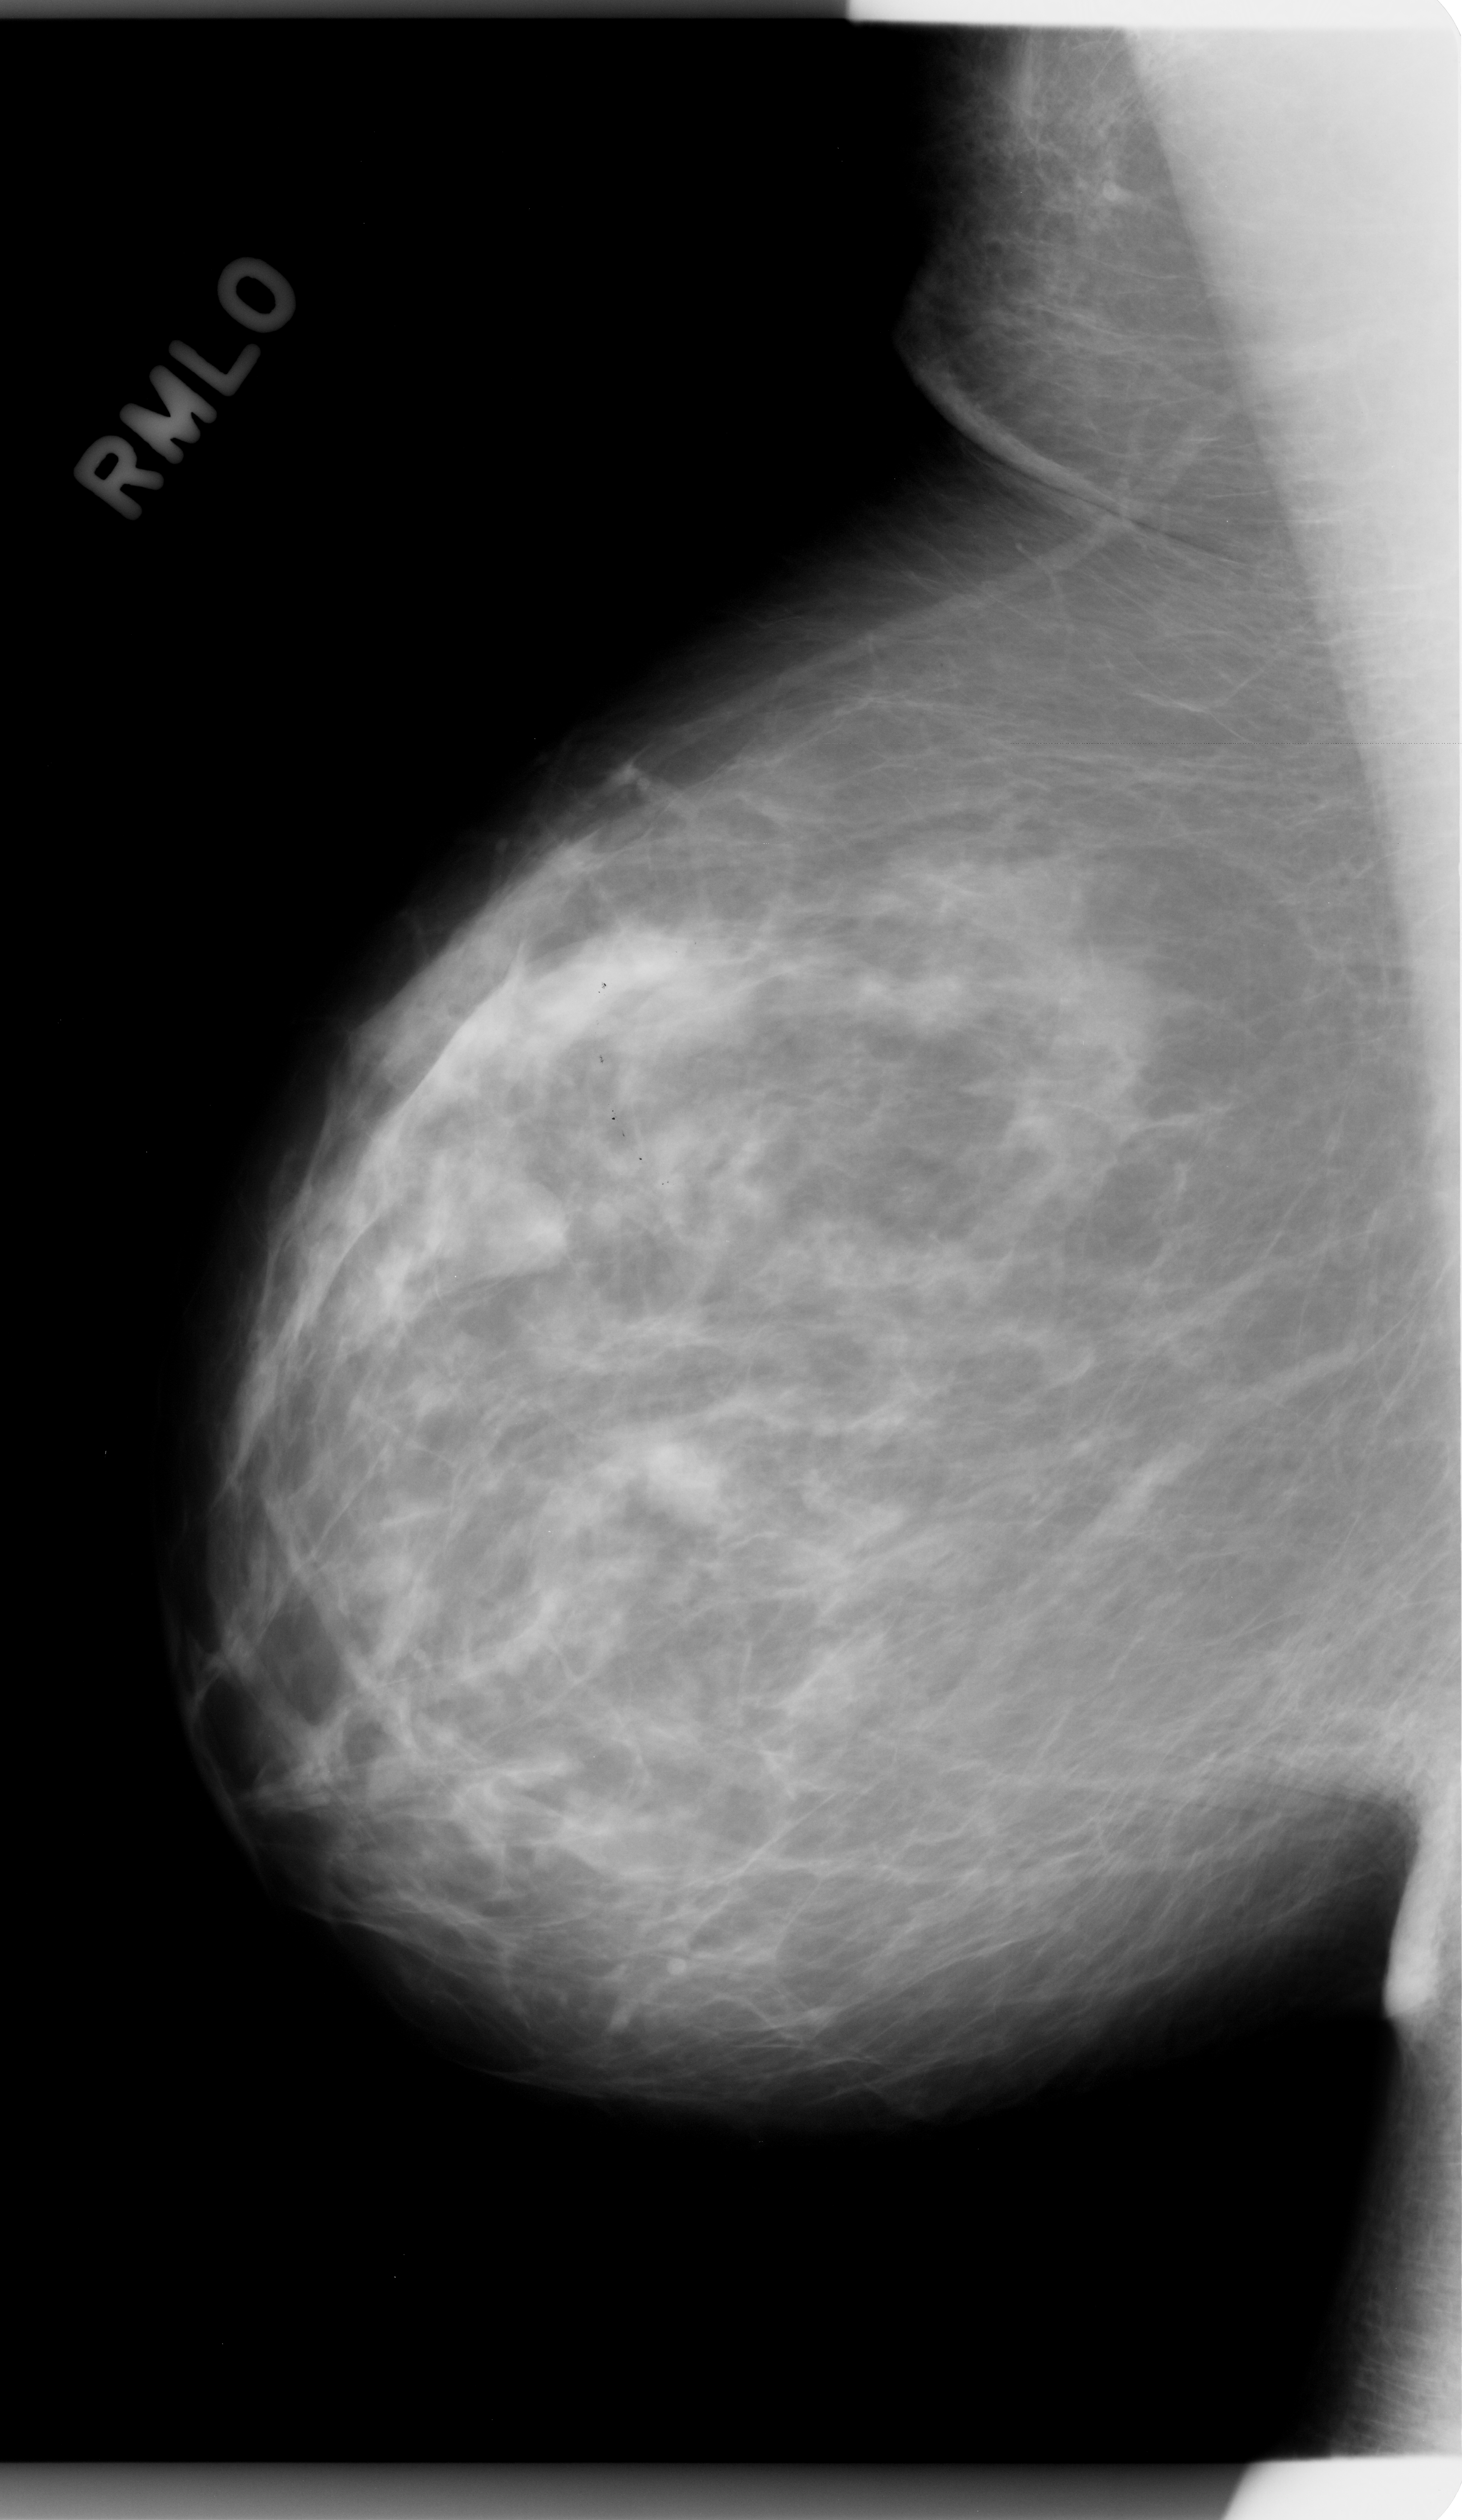
Mammogram (digitized film), right breast, MLO view, BI-RADS breast density category 2 (scale 1–4).
Marked findings (only marked abnormalities are described; nothing is implied about the rest of the image): mass, shape round, margins obscured; BI-RADS assessment category 3; subtlety rating 4 on a 1 (subtle) to 5 (obvious) scale; pathology result (as recorded, not read from the image): benign.